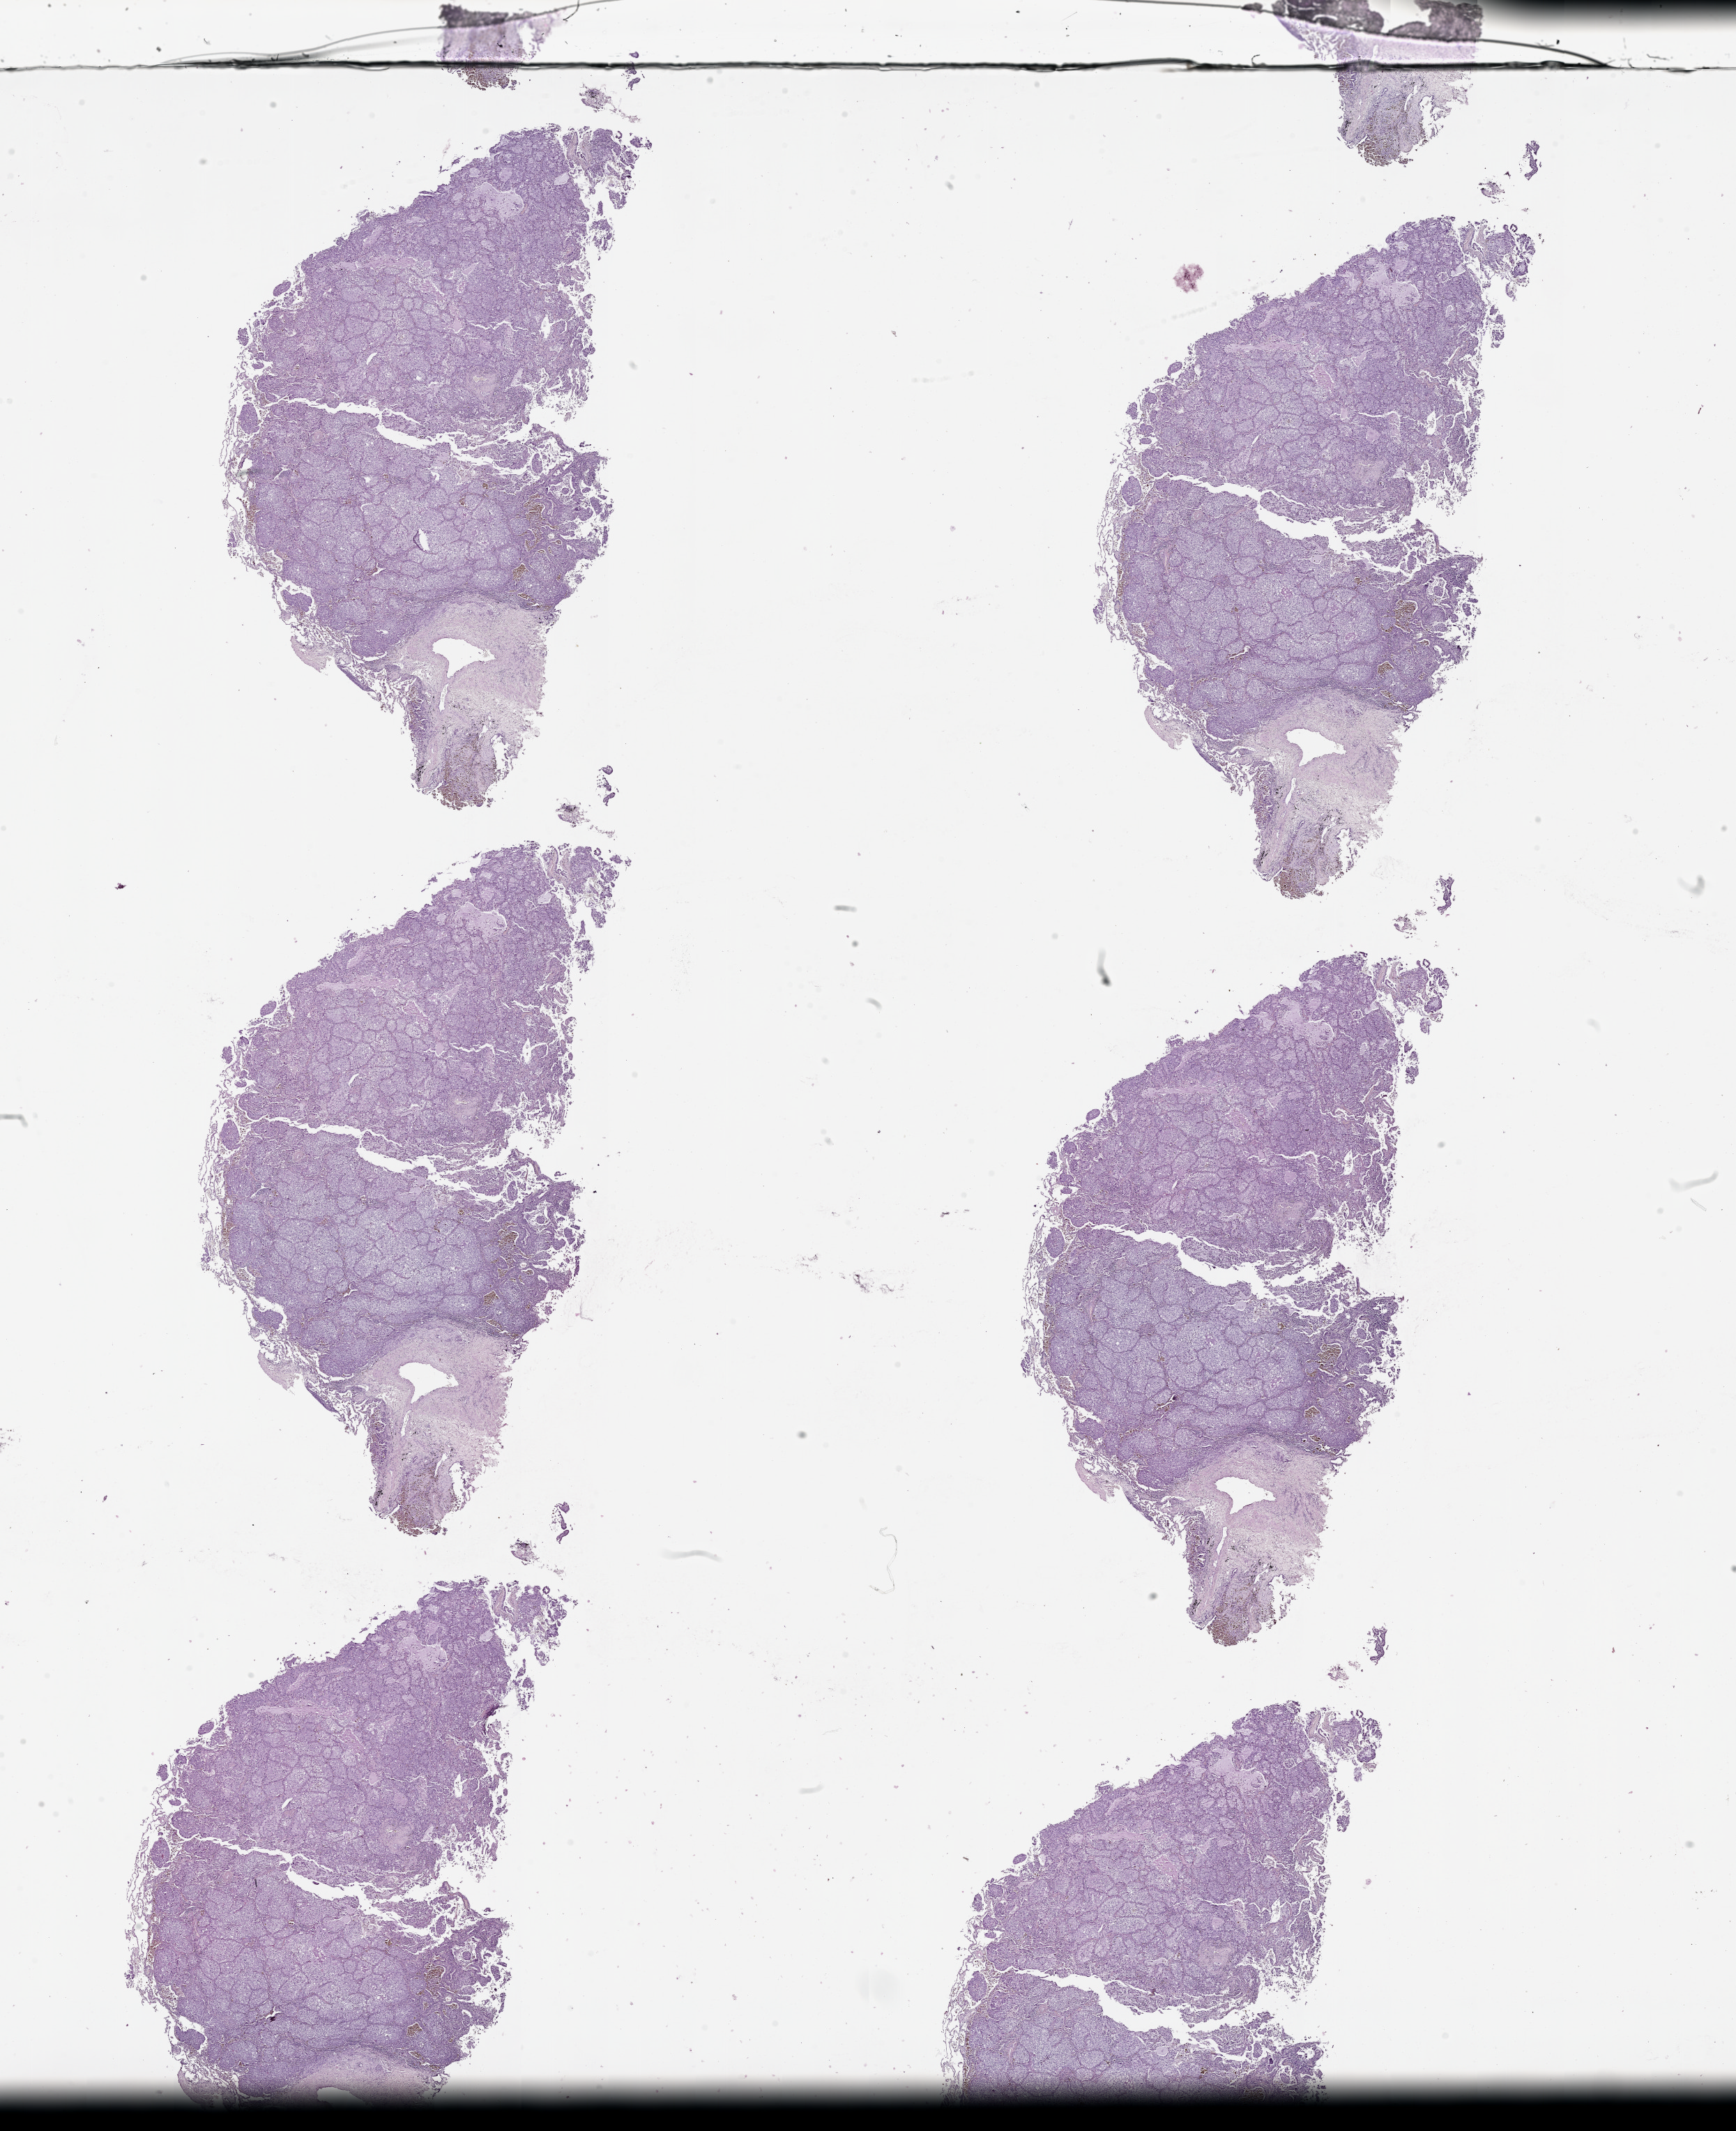
Whole-slide histology image, H&E, low-resolution overview of the scanned area, about 20.0 x 24.6 mm. Lung, tissue type not recorded.
Patient diagnosis (cohort enrolment): lung adenocarcinoma (lung).